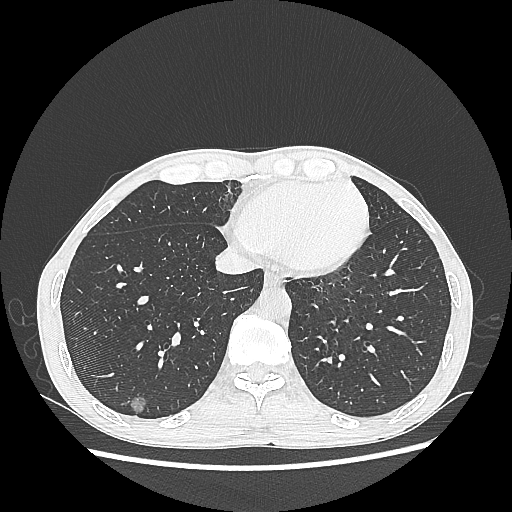
Chest CT, one axial slice; position 79 of 270 along the scan axis; 100 kVp; lung window (W 1500 / L -600 HU); 512 × 512 image matrix, field of view 360 × 360 mm. Male patient, age 60 years. From the clinical record (not read from this slice): clinical TNM (as recorded): T1c N0 M0; histopathological grade: G2.
Annotated regions visible in this slice (bounding box drawn by a radiologist):
- lung tumour (recorded histology: adenocarcinoma): bounding box (x1, y1, x2, y2) in pixels: (122, 392, 148, 418)